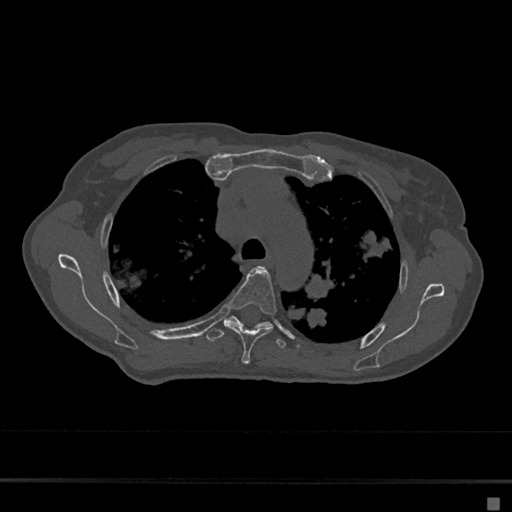
CT including the spine, one axial slice. Slice 491 of 797 in the series (ordered by position). Reconstruction kernel Br40s/3. Bone window (W 1800 / L 400 HU). 0.5 mm slice thickness. 512 × 512 image matrix, field of view 360 × 360 mm. Female patient, age 68 years. Case-level facts recorded for this patient, not image findings: primary cancer: renal.
Annotated regions visible in this slice (semi-automatic segmentation, software-assisted and operator-edited):
- T4 vertebra: bounding box (x1, y1, x2, y2) in pixels: (224, 267, 276, 364)
- T5 vertebra: (206, 316, 287, 349)